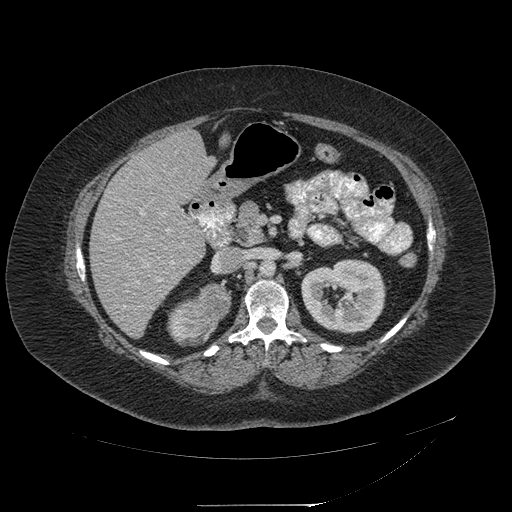
Contrast-enhanced abdominal CT, one axial slice; position 112 of 217 along the scan axis; reconstruction kernel STANDARD; intravenous contrast given; soft-tissue window (W 400 / L 40 HU); 1.25 mm slice thickness; 512 × 512 image matrix. Female patient, age 55 years. Case-level facts recorded for this patient, not image findings: diagnosis: adrenocortical carcinoma; tumour side: right adrenal; tumour size at pathology: 11 cm; Ki-67 index: 20 %; stage (as recorded): 2.
Structures marked on this image (semi-automatically segmented with operator editing):
- mass: bounding box (x1, y1, x2, y2) in pixels: (178, 286, 227, 333)